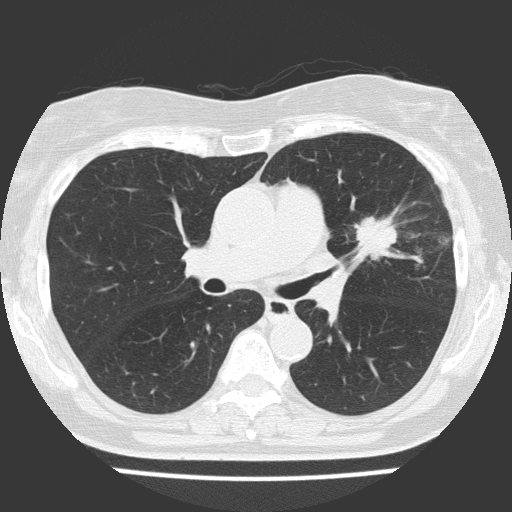
Low-dose screening chest CT, one axial slice. Position 88 of 151 along the scan axis. Lung window (W 1500 / L -600 HU). 2 mm slice thickness. 512 × 512 image matrix, field of view 309 × 309 mm.
Outlined on this slice (expert manual segmentation):
- lesion 1 (tumor, upper lobe of left lung): bounding box [x1, y1, x2, y2] px = [354, 217, 397, 260]